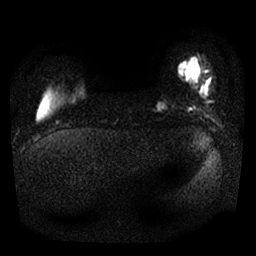
Breast MRI, one axial slice. Diffusion-weighted series; image 2 of 4 stored at this slice position (different b-values; order by instance number). 1.5 T. 4 mm slice thickness. 256 × 256 image matrix, field of view 300 × 300 mm. Female patient.
Outlined on this slice (outlined manually by an expert reader):
- tumour on diffusion-weighted imaging: bounding box (x1, y1, x2, y2) in pixels: (159, 103, 165, 107)